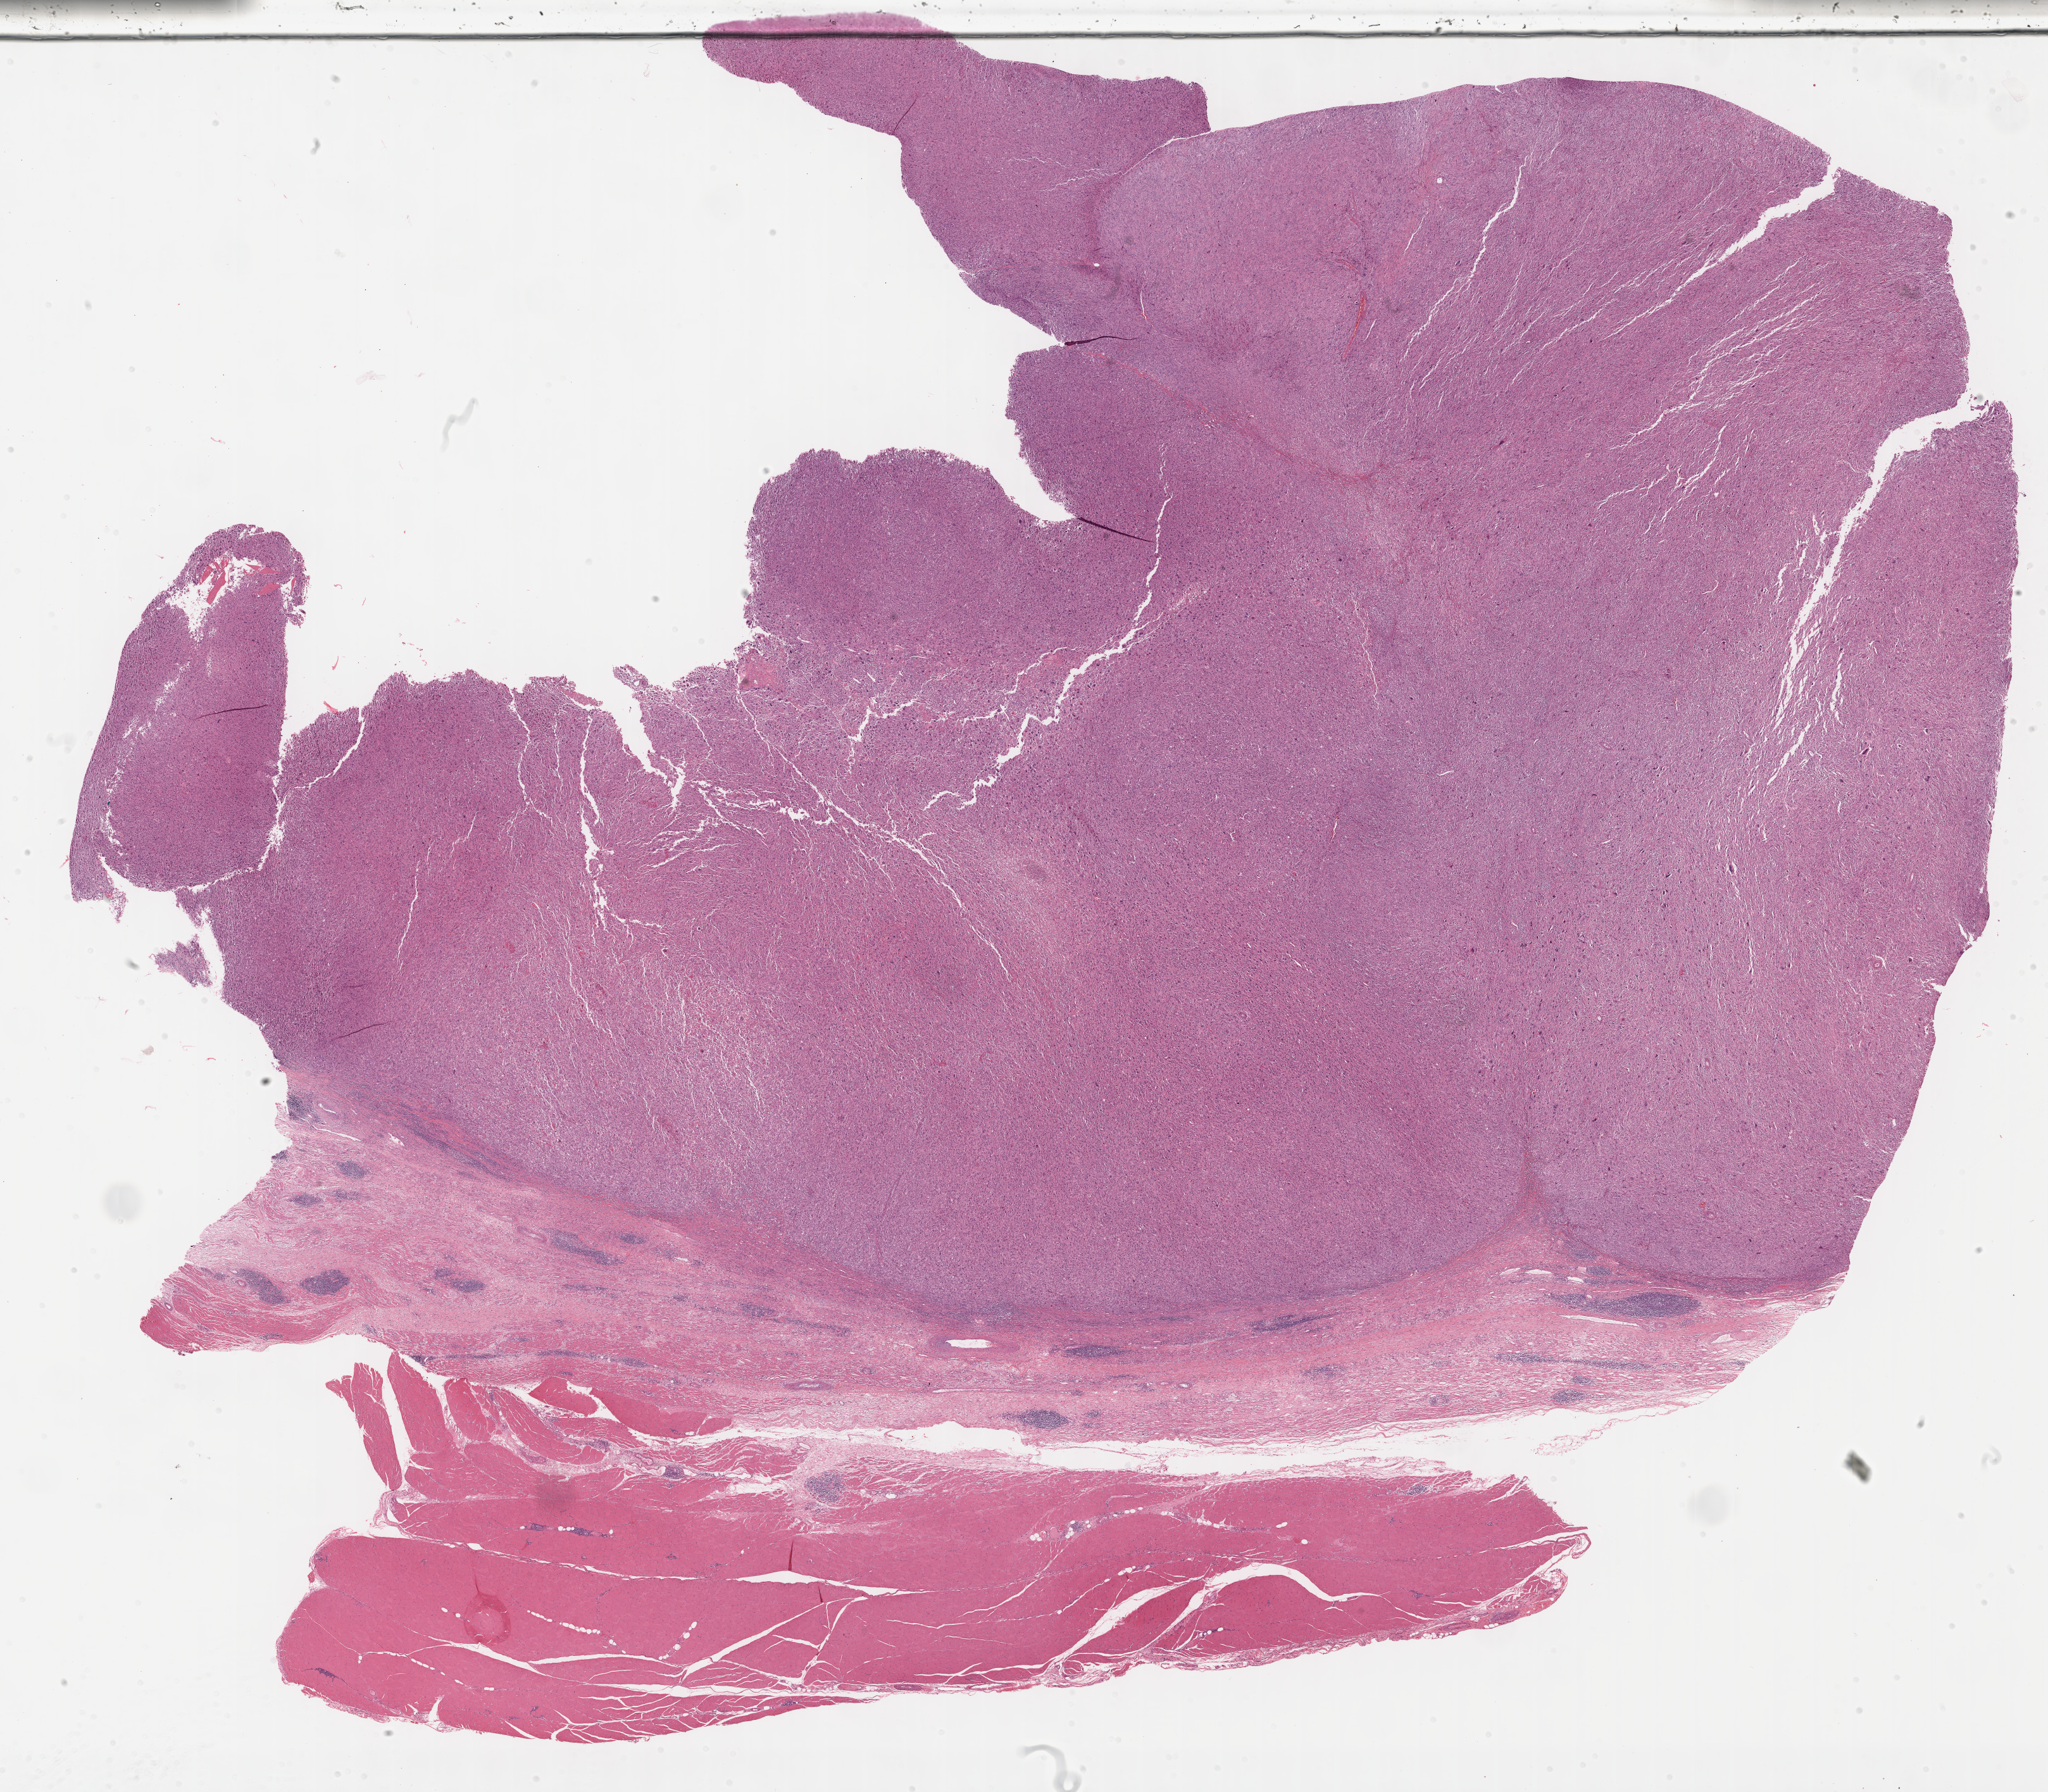
Digitized H&E-stained tissue section (whole slide), a low-resolution overview of the entire scanned area, about 26.2 x 22.9 mm (from a 40x scan); formalin-fixed paraffin-embedded (FFPE) diagnostic section; sample: primary tumour, connective, subcutaneous and other soft tissues. Female, age 62 years at initial diagnosis.
Diagnosis: Malignant fibrous histiocytoma (connective, subcutaneous and other soft tissues of lower limb and hip).